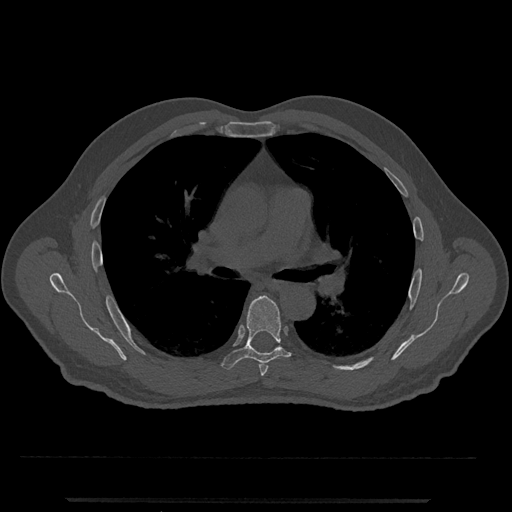
CT including the spine, one axial slice. Position 745 of 797 along the scan axis. 120 kVp. Bone window (W 1800 / L 400 HU). 0.5 mm slice thickness. 512 × 512 image matrix, field of view 419 × 419 mm. Patient: male, 63 years. Case-level facts recorded for this patient, not image findings: primary cancer: prostate.
Structures marked on this image (semi-automatically segmented with operator editing):
- T5 vertebra: bounding box [x1, y1, x2, y2] px = [259, 363, 268, 376]
- T6 vertebra: [222, 296, 303, 370]